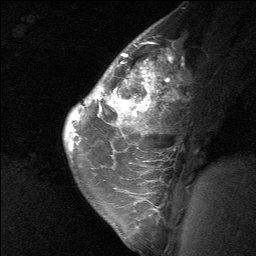
Breast MRI (dynamic contrast-enhanced), one sagittal slice. Dynamic contrast-enhanced study with each time point stored as its own series, time point 2 of 3 at this slice position (early post-contrast, ordered by acquisition time). 1.5 T. TE 4.8 ms, TR 27 ms. 2 mm slice thickness. 256 × 256 image matrix, field of view 180 × 180 mm. Female patient, age 26 years. Case-level facts recorded for this patient, not image findings: setting: breast cancer imaged before/during neoadjuvant chemotherapy; receptor status: HR-positive, HER2-negative.
Annotated regions visible in this slice (semi-automatic segmentation, software-assisted and operator-edited):
- analysis volume of interest (the breast-tissue region the enhancement analysis was run in; not a lesion): bounding box [x1, y1, x2, y2] px = [86, 43, 175, 138]
- tumour enhancement mask (voxels above the 90 % enhancement threshold inside the analysis volume of interest): [98, 54, 158, 116]